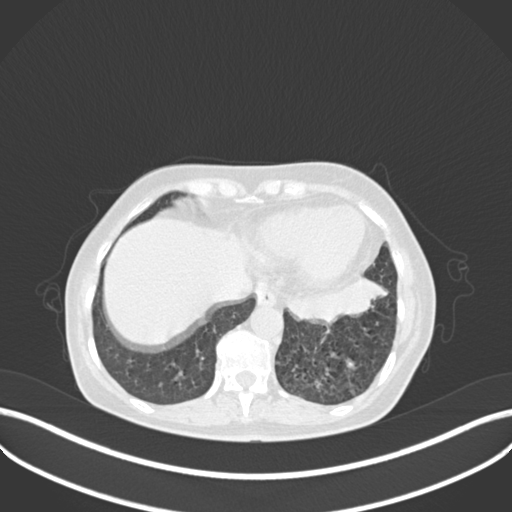
Chest CT, one axial slice; slice 58 of 270 in the series (ordered by position); reconstruction kernel B30f; 120 kVp; lung window (W 1500 / L -600 HU); 512 × 512 image matrix, field of view 400 × 400 mm. Patient: female, 63 years. From the clinical record (not read from this slice): clinical TNM (as recorded): T1b N0 M0.
Outlined on this slice (rectangle marked by the reading radiologist):
- lung tumour (recorded histology: adenocarcinoma): bounding box <284,273,390,326> (left, top, right, bottom; pixels)